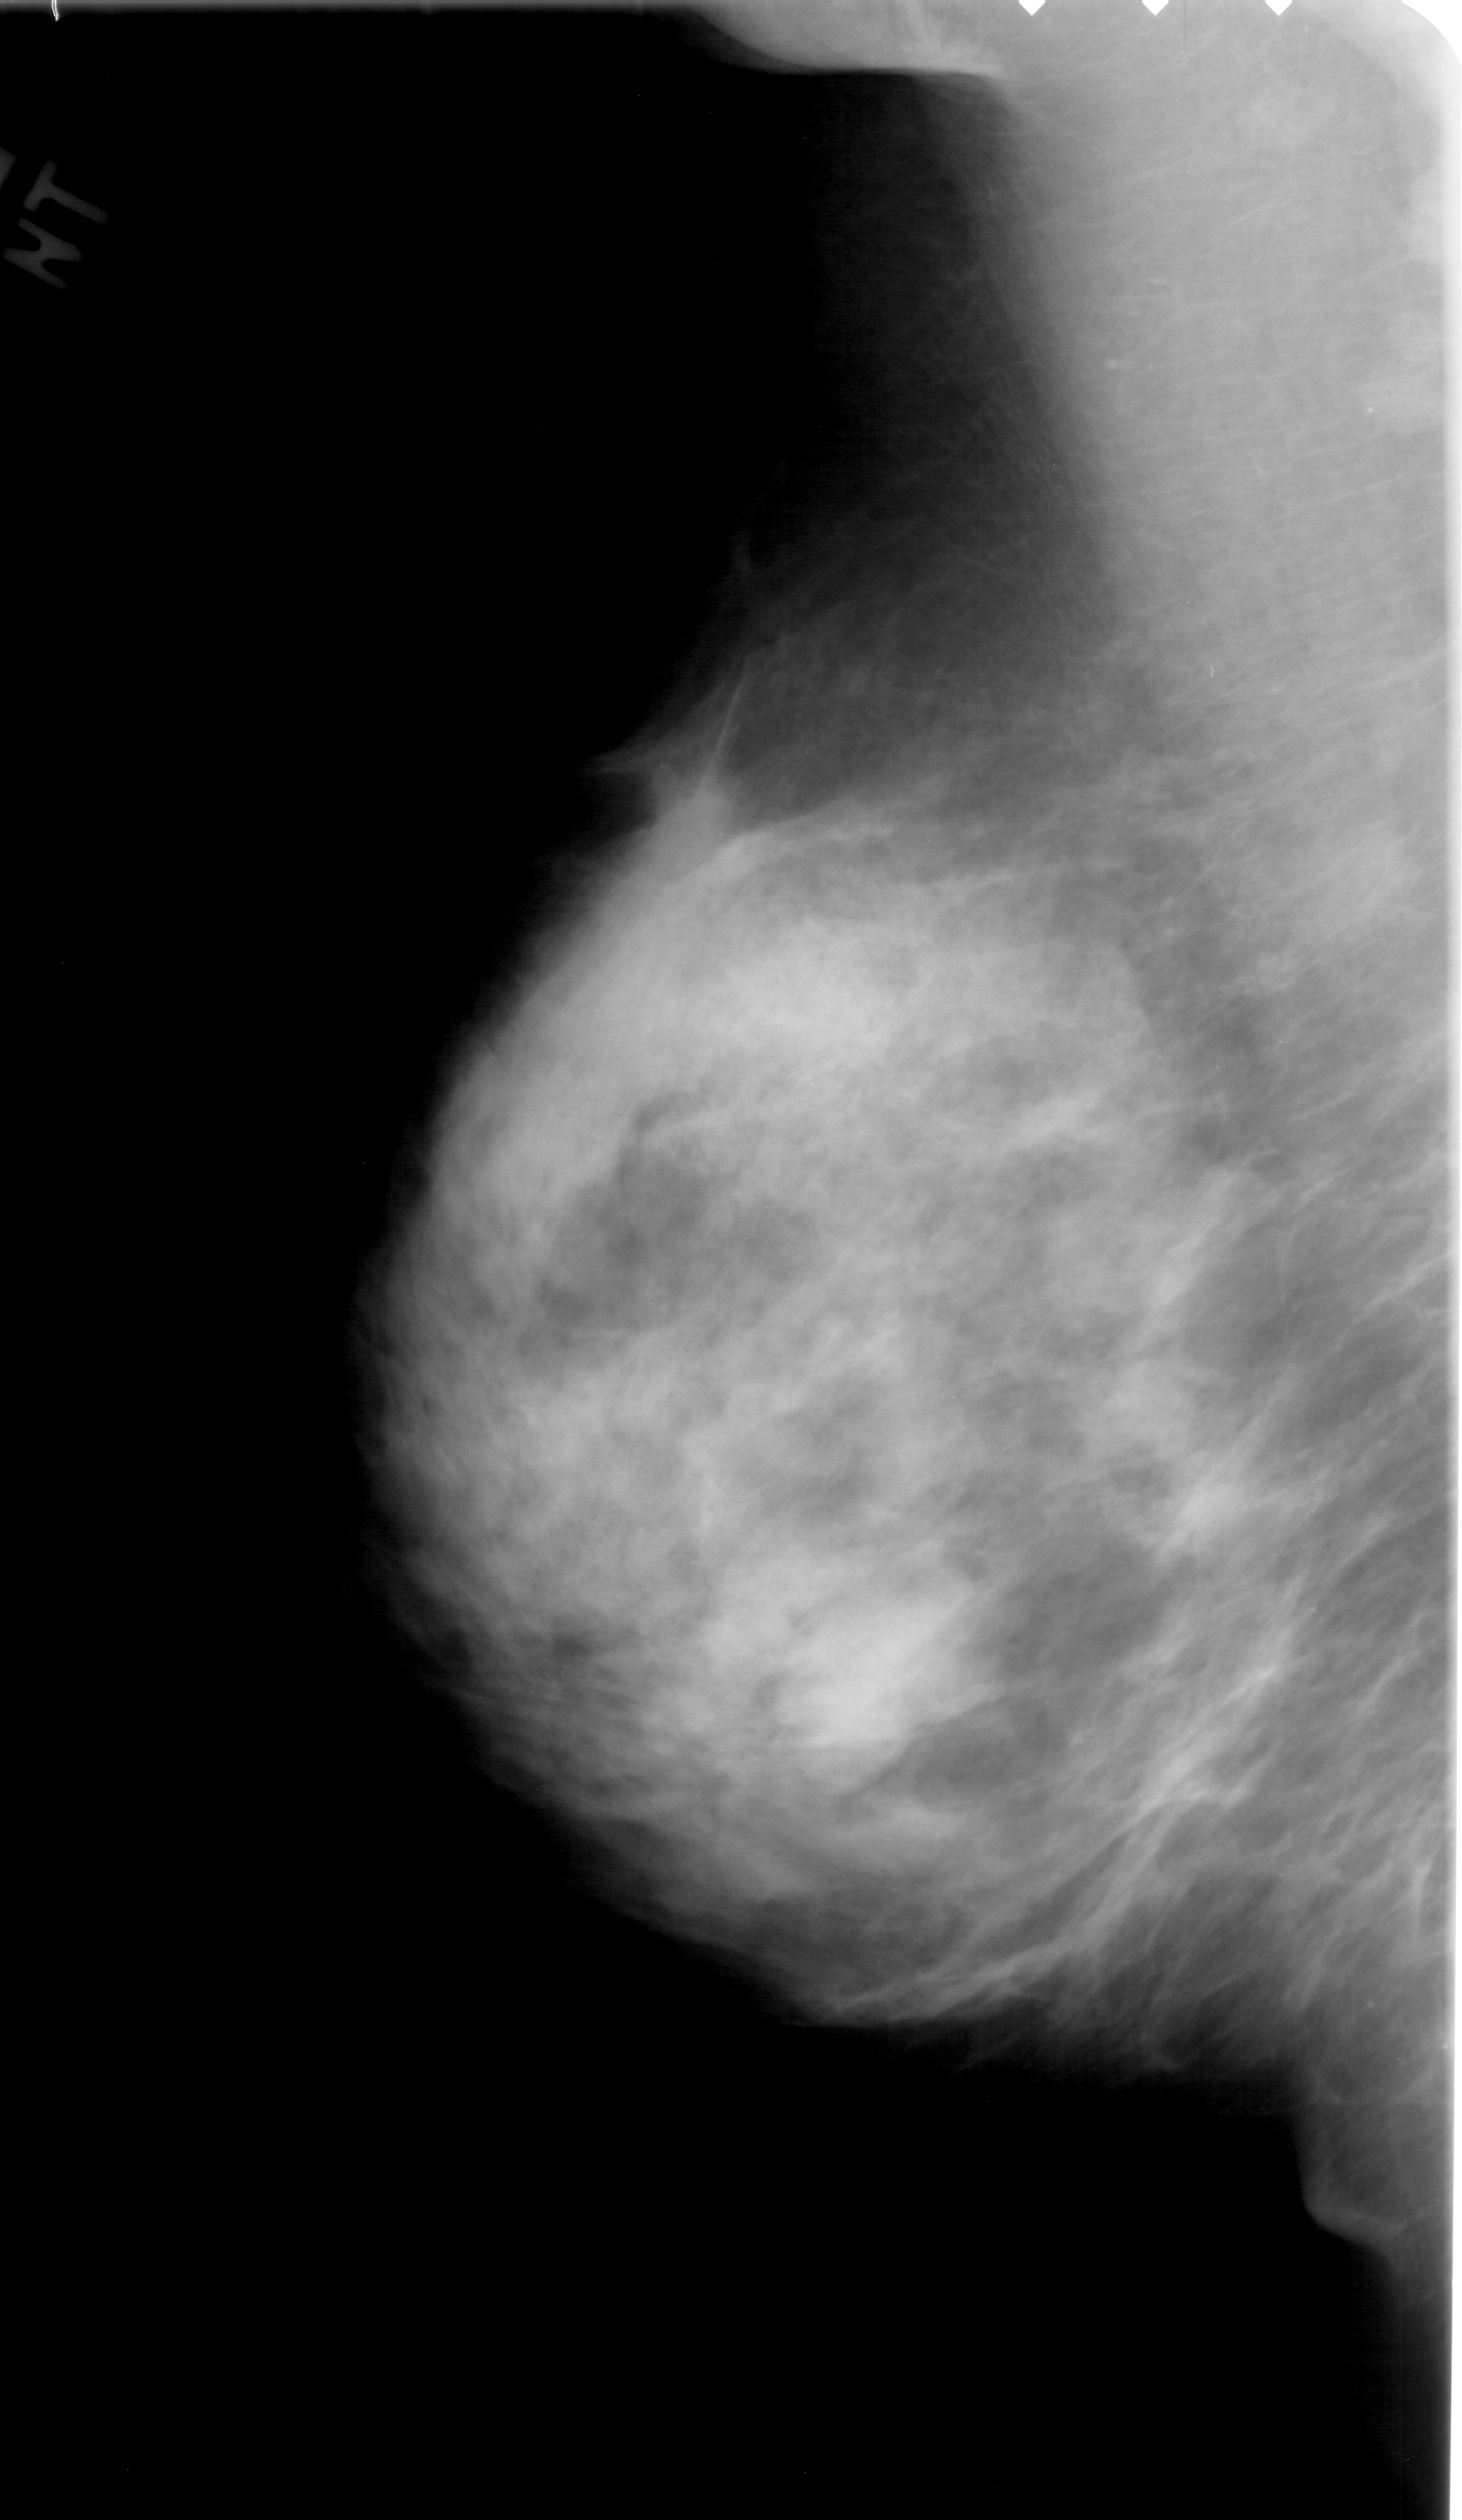
Digitized screen-film mammogram, left breast, mediolateral oblique (MLO) view.
- Marked findings (only marked abnormalities are described; nothing is implied about the rest of the image): mass, shape lobulated, margins obscured; BI-RADS assessment category 4; pathology result (as recorded, not read from the image): benign.